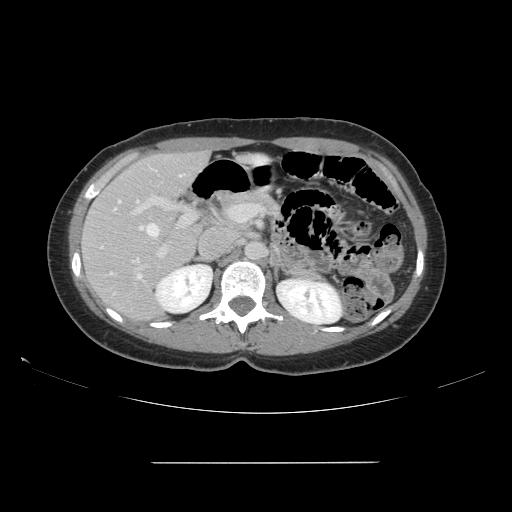
Contrast-enhanced abdominal CT, one axial slice. Position 90 of 151 along the scan axis. 120 kVp. Intravenous contrast given. Soft-tissue window (W 400 / L 40 HU). 512 × 512 image matrix. Female patient, age 46 years. Case-level facts recorded for this patient, not image findings: diagnosis: colorectal cancer liver metastases, imaged before liver resection; multiple liver metastases: yes.
Annotated regions visible in this slice (expert manual segmentation):
- hepatic veins: bounding box (x1, y1, x2, y2) in pixels: (111, 175, 183, 278)
- liver: (83, 152, 208, 322)
- planned liver remnant (the part of the liver to remain after resection): (92, 153, 202, 274)
- portal vein (with intrahepatic branches): (131, 181, 247, 272)